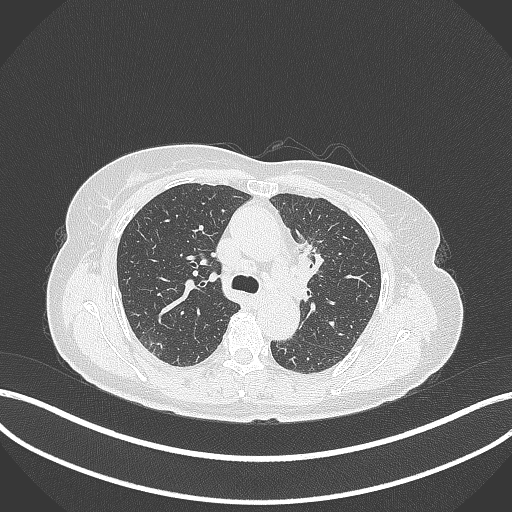
Chest CT, one axial slice. Position 225 of 369 along the scan axis. Lung window (W 1500 / L -600 HU). 1 mm slice thickness. 512 × 512 image matrix, field of view 400 × 400 mm. Female patient, age 65 years. From the clinical record (not read from this slice): clinical TNM (as recorded): T2a N0 M0; histopathological grade: G2-3.
Outlined on this slice (rectangle marked by the reading radiologist):
- lung tumour (recorded histology: adenocarcinoma): box from (x=293, y=233) to (x=327, y=278) px